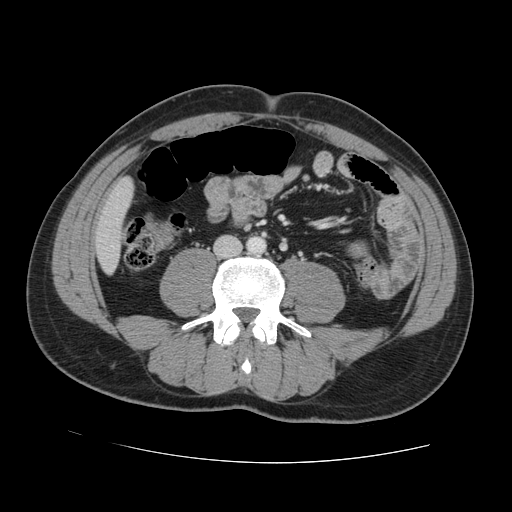
Contrast-enhanced abdominal CT, one axial slice; position 15 of 131 along the scan axis; soft-tissue window (W 400 / L 40 HU); 2.5 mm slice thickness; 512 × 512 image matrix, field of view 380 × 380 mm. Male patient, age 40 years. Case-level facts recorded for this patient, not image findings: diagnosis: colorectal cancer liver metastases, imaged before liver resection.
Annotated regions visible in this slice (expert manual segmentation):
- liver: bounding box <96,181,133,271> (left, top, right, bottom; pixels)